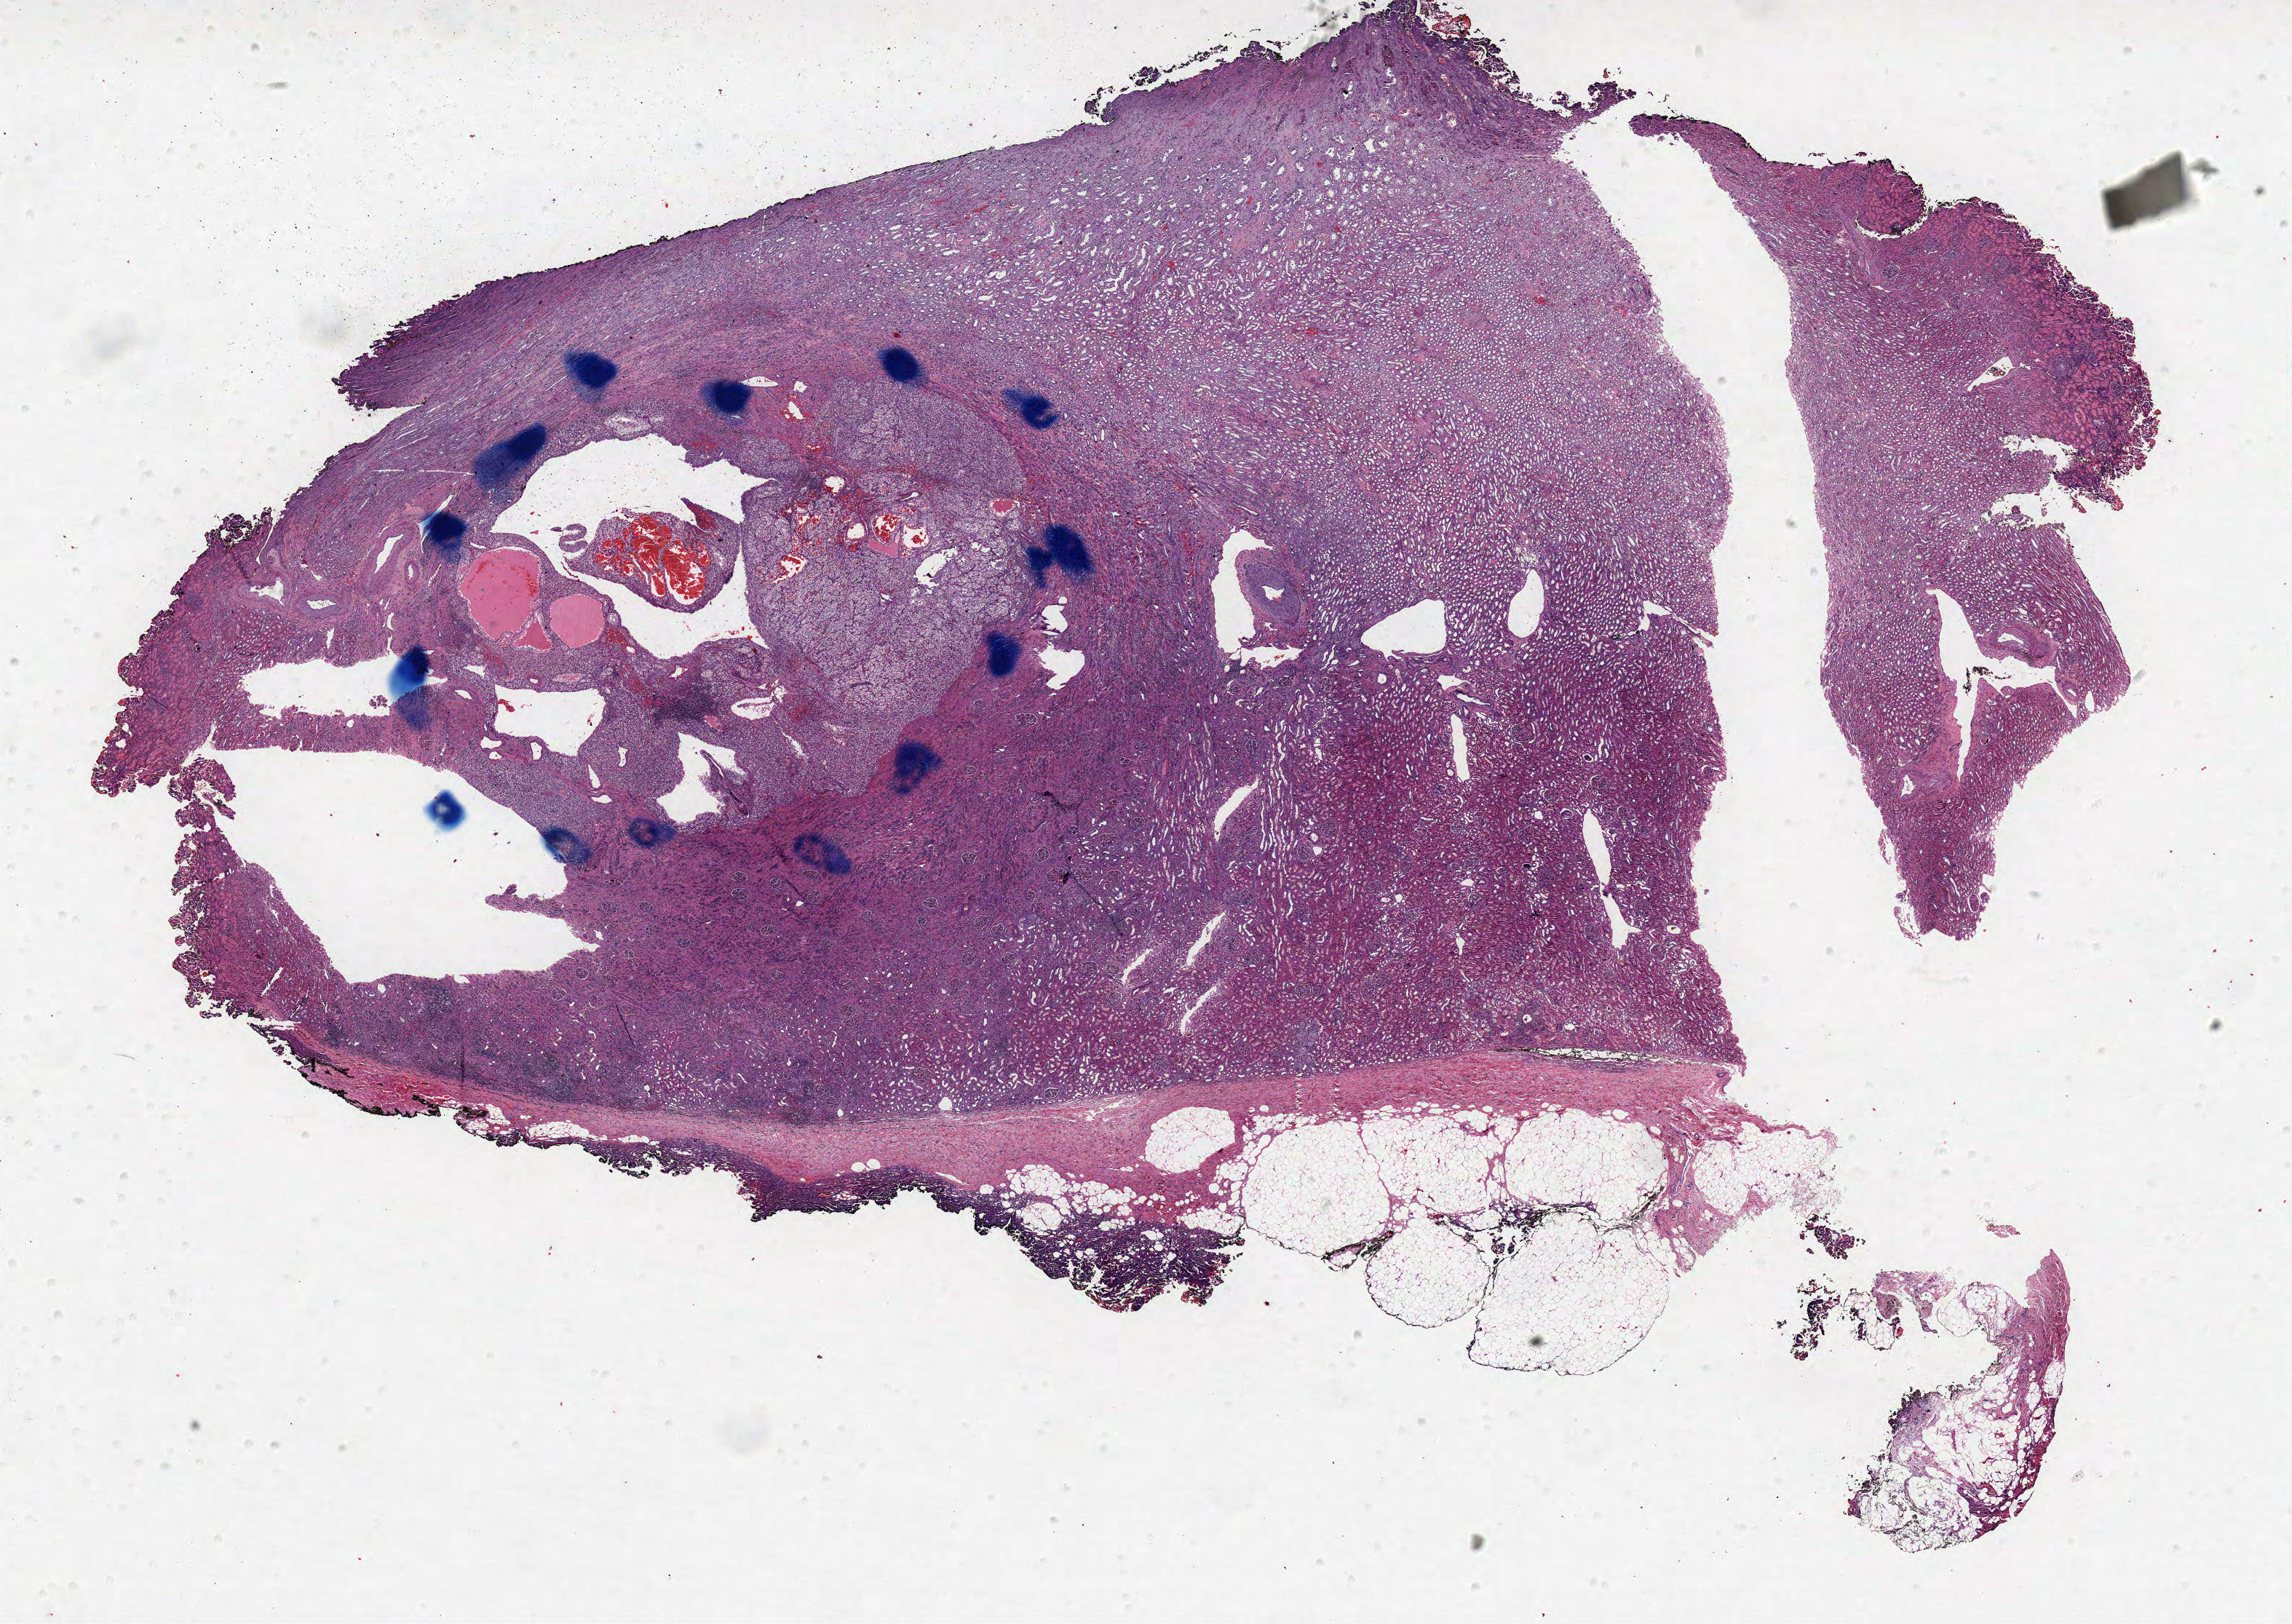
Hematoxylin and eosin (H&E) stained whole-slide image, whole scanned area (about 25.2 x 17.8 mm, acquisition: 40x scan) shown as a low-resolution overview, formalin-fixed paraffin-embedded (FFPE) diagnostic section, primary tumour sample from the kidney. Male, age 42 years at initial diagnosis. Histologic grade: G3 (poorly differentiated).
- laterality: left
- AJCC pathologic stage: I
- diagnosis: Clear cell adenocarcinoma, NOS